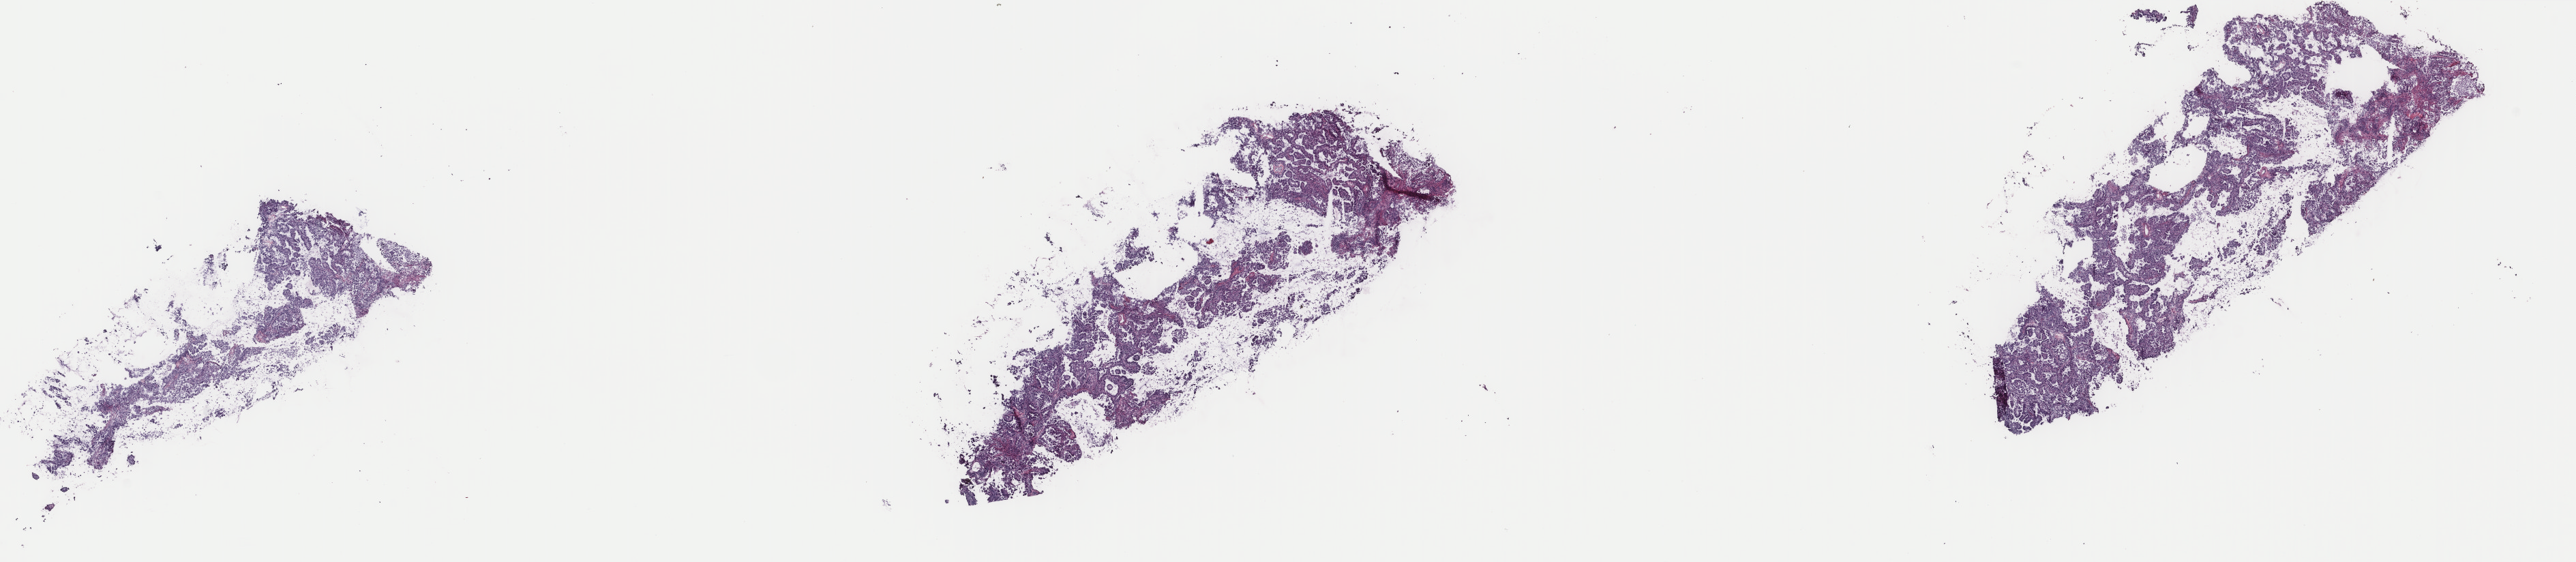
Digitized Hematoxylin and eosin (H&E) stained tissue section (whole slide), low-resolution overview of the scanned area, about 30.0 x 6.5 mm; frozen section; sample: primary tumour, lung. Male patient; age at initial diagnosis 73 years. Slide review estimates, as recorded: tumour cells 100%, tumour nuclei 75%, normal cells 0%, stromal cells 0%, necrosis 0%. Inflammatory infiltration, as recorded: lymphocyte infiltration 3%, monocyte infiltration 2%, neutrophil infiltration 0%.
- AJCC pathologic stage: IB (6th edition)
- histologic diagnosis: Papillary adenocarcinoma, NOS (upper lobe, lung)